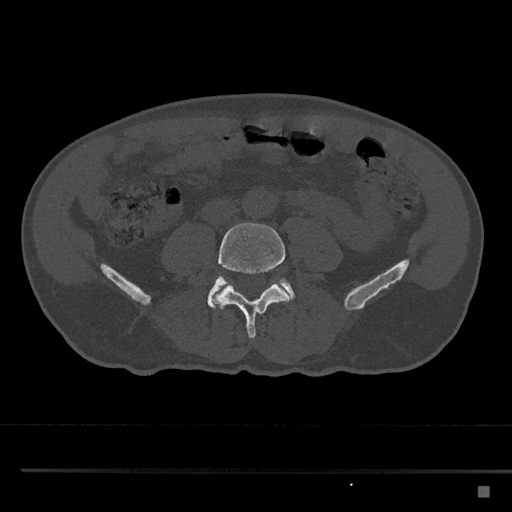
CT including the spine, one axial slice; reconstruction kernel Br40s/3; 120 kVp; bone window (W 1800 / L 400 HU); 0.5 mm slice thickness; 512 × 512 image matrix. Patient: male, 59 years. From the clinical record (not read from this slice): primary cancer: prostate.
Outlined on this slice (semi-automatically segmented with operator editing):
- L4 vertebra: bounding box [x1, y1, x2, y2] px = [213, 223, 290, 338]
- L5 vertebra: [207, 276, 295, 309]